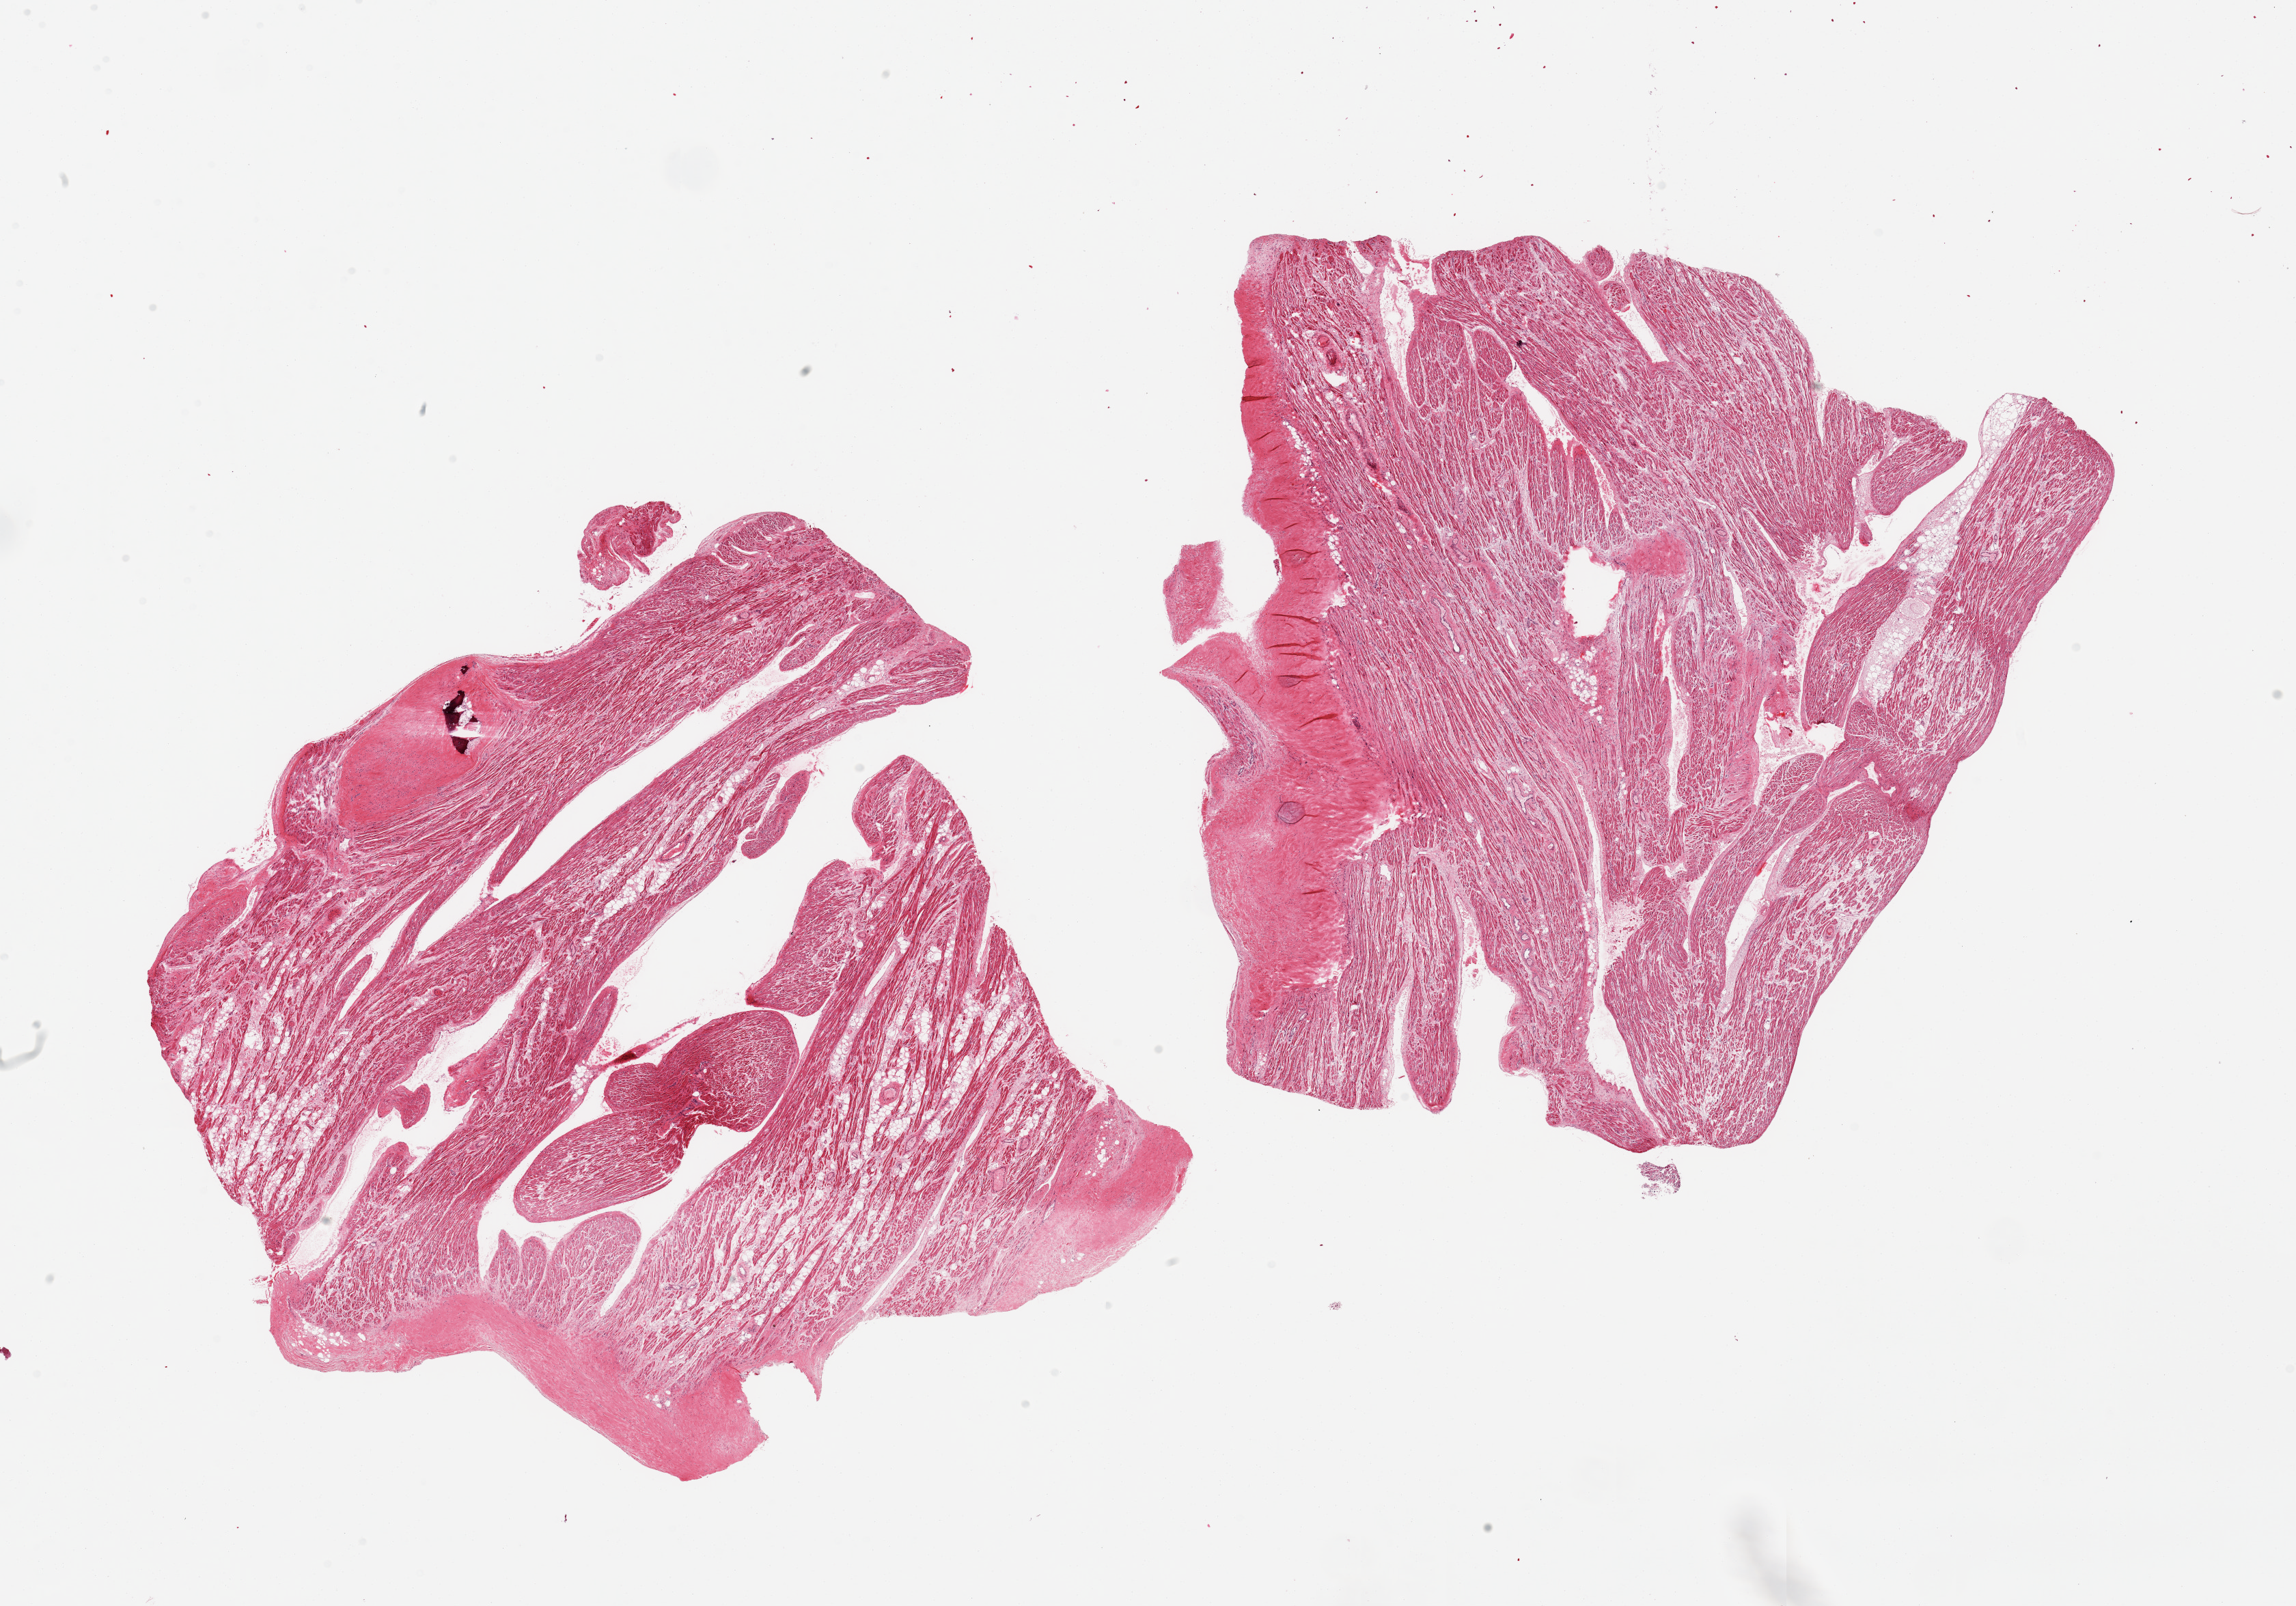
Digitized H&E-stained section, low-resolution overview of the scanned area, about 26.6 x 18.6 mm; PAXgene-fixed, paraffin-embedded tissue; section of auricular appendage (target tissue); tissue donor sample. Male donor.
Pathologist's review note for this sample: 2 pieces cerebellum.